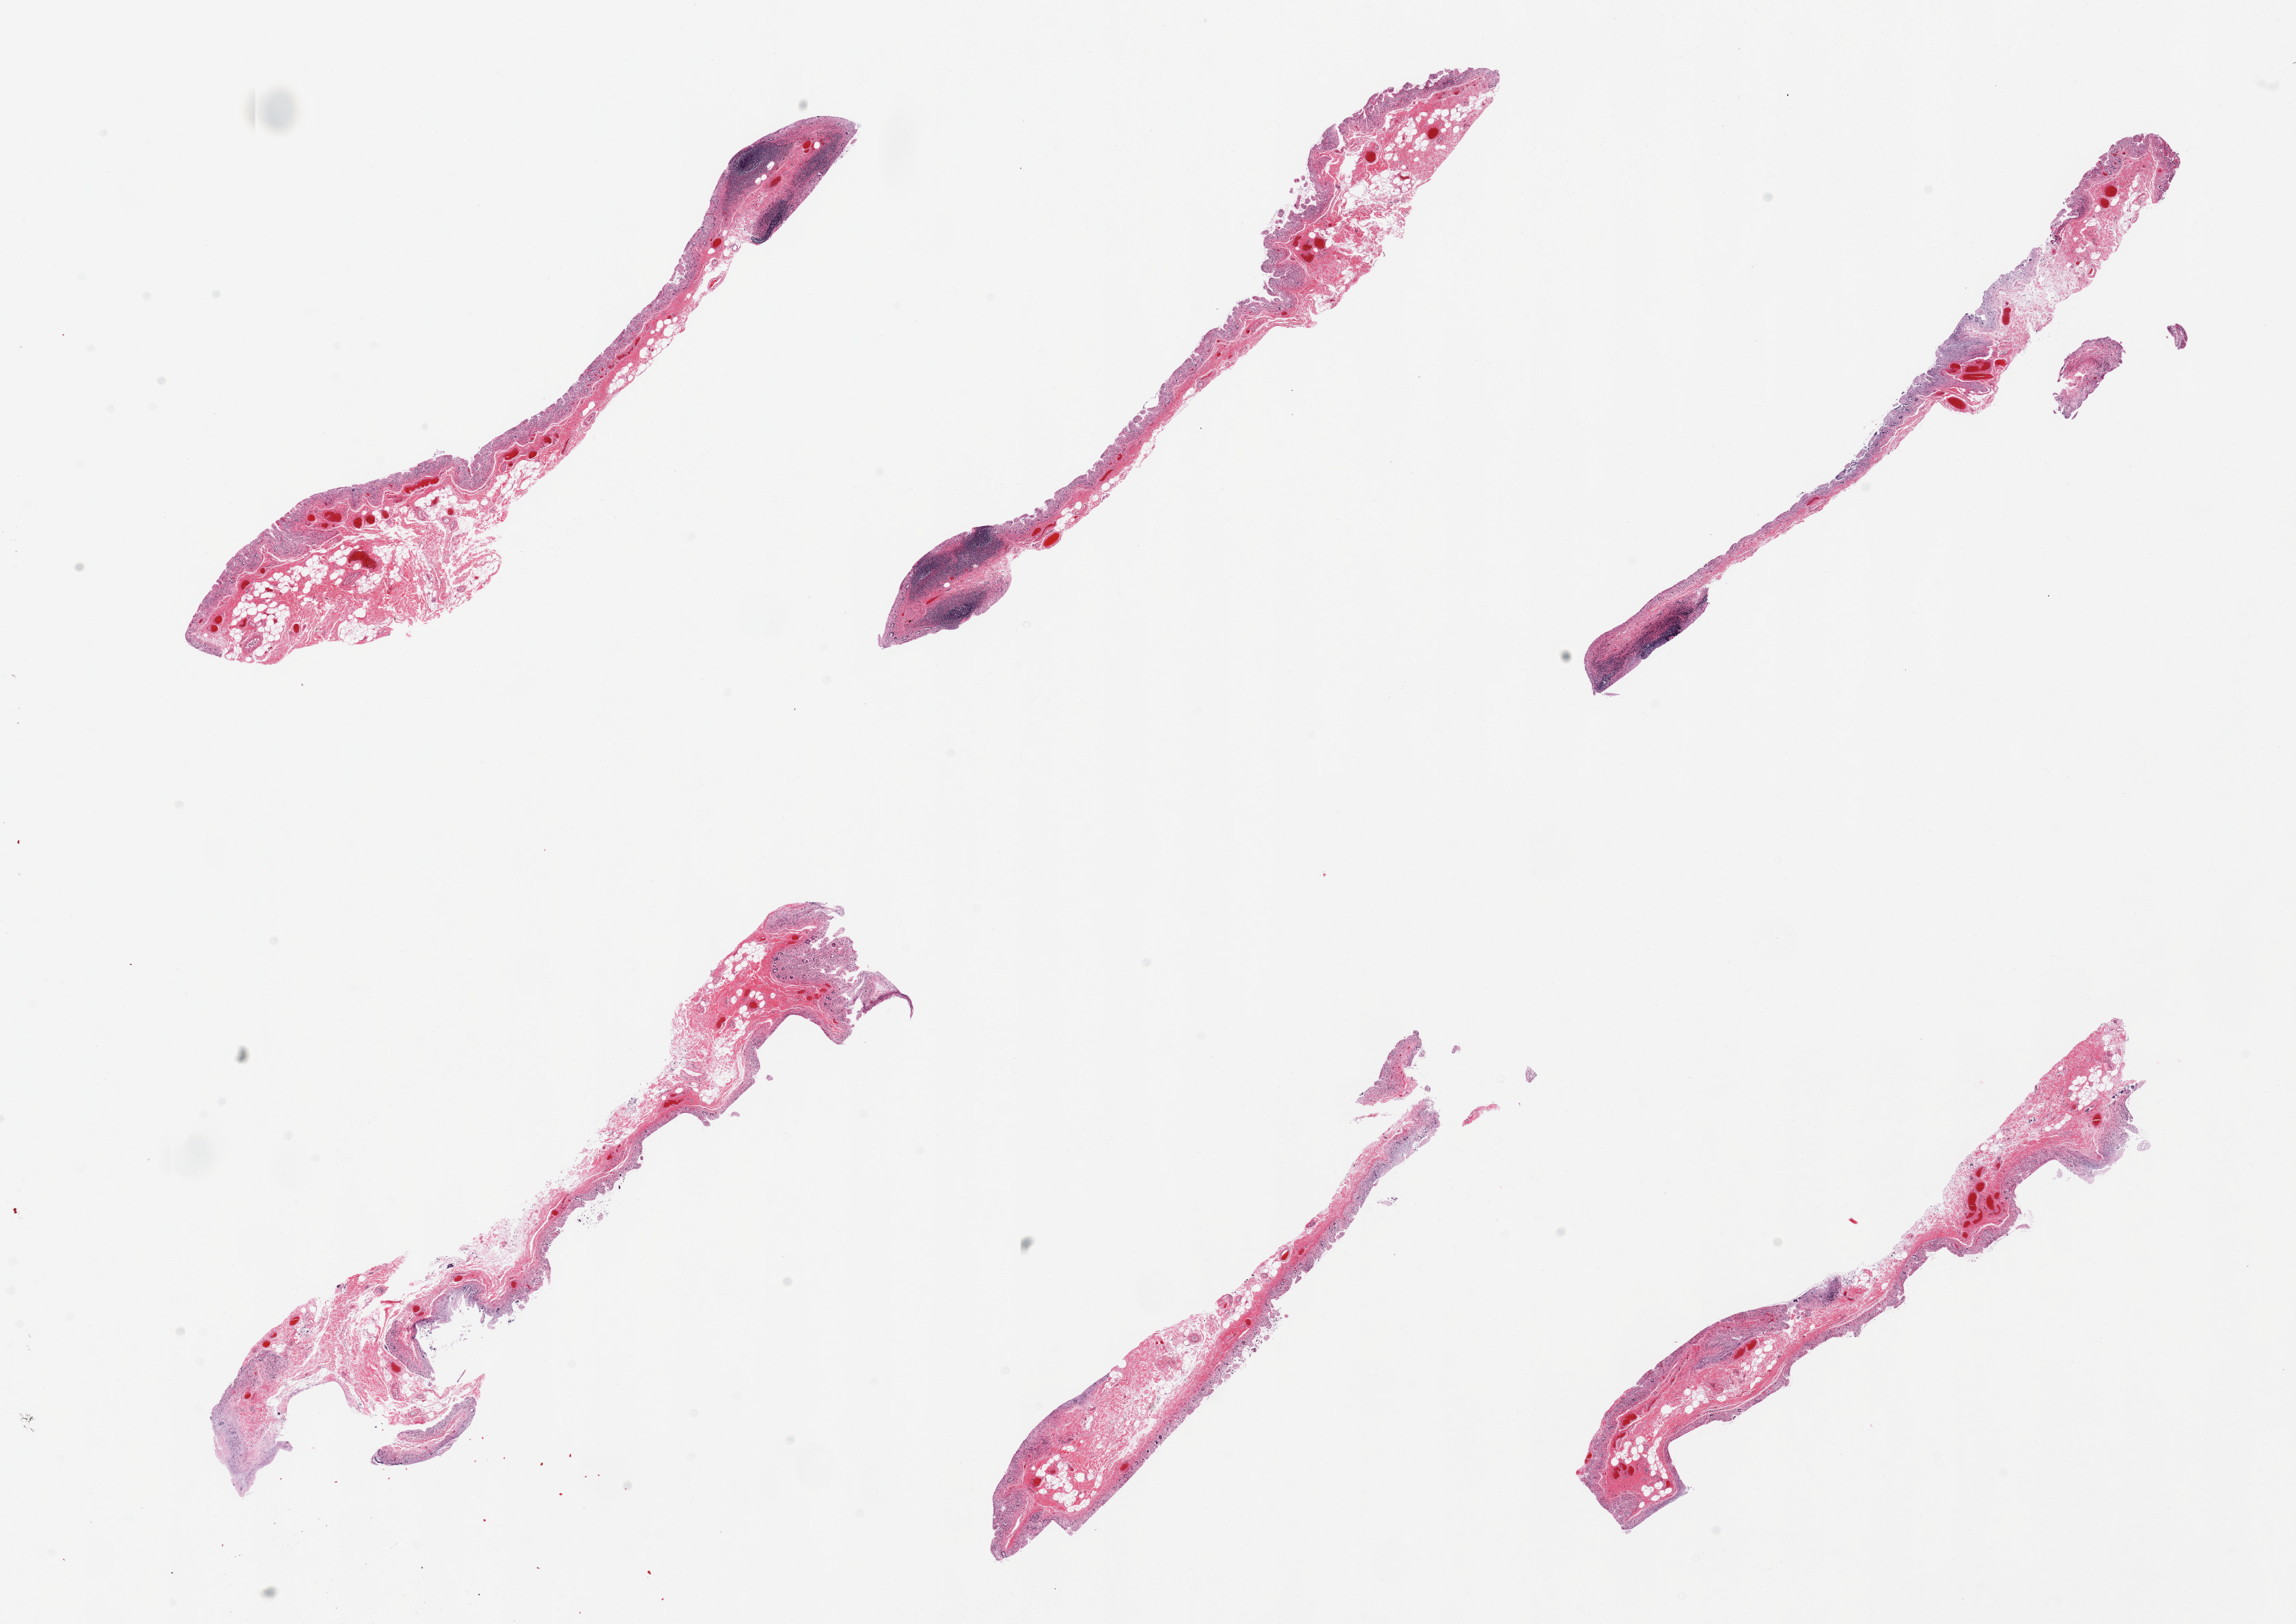
Digitized haematoxylin and eosin-stained section, brightfield, a low-resolution overview of the entire scanned area, about 26.6 x 18.8 mm; PAXgene-fixed paraffin-embedded (PFPE) section; target tissue: ileum; tissue donor sample. Donor: male.
Reviewer comment on this tissue sample: 4 pieces, mucosa autolzyed, ~10% lymphoid aggregateds.